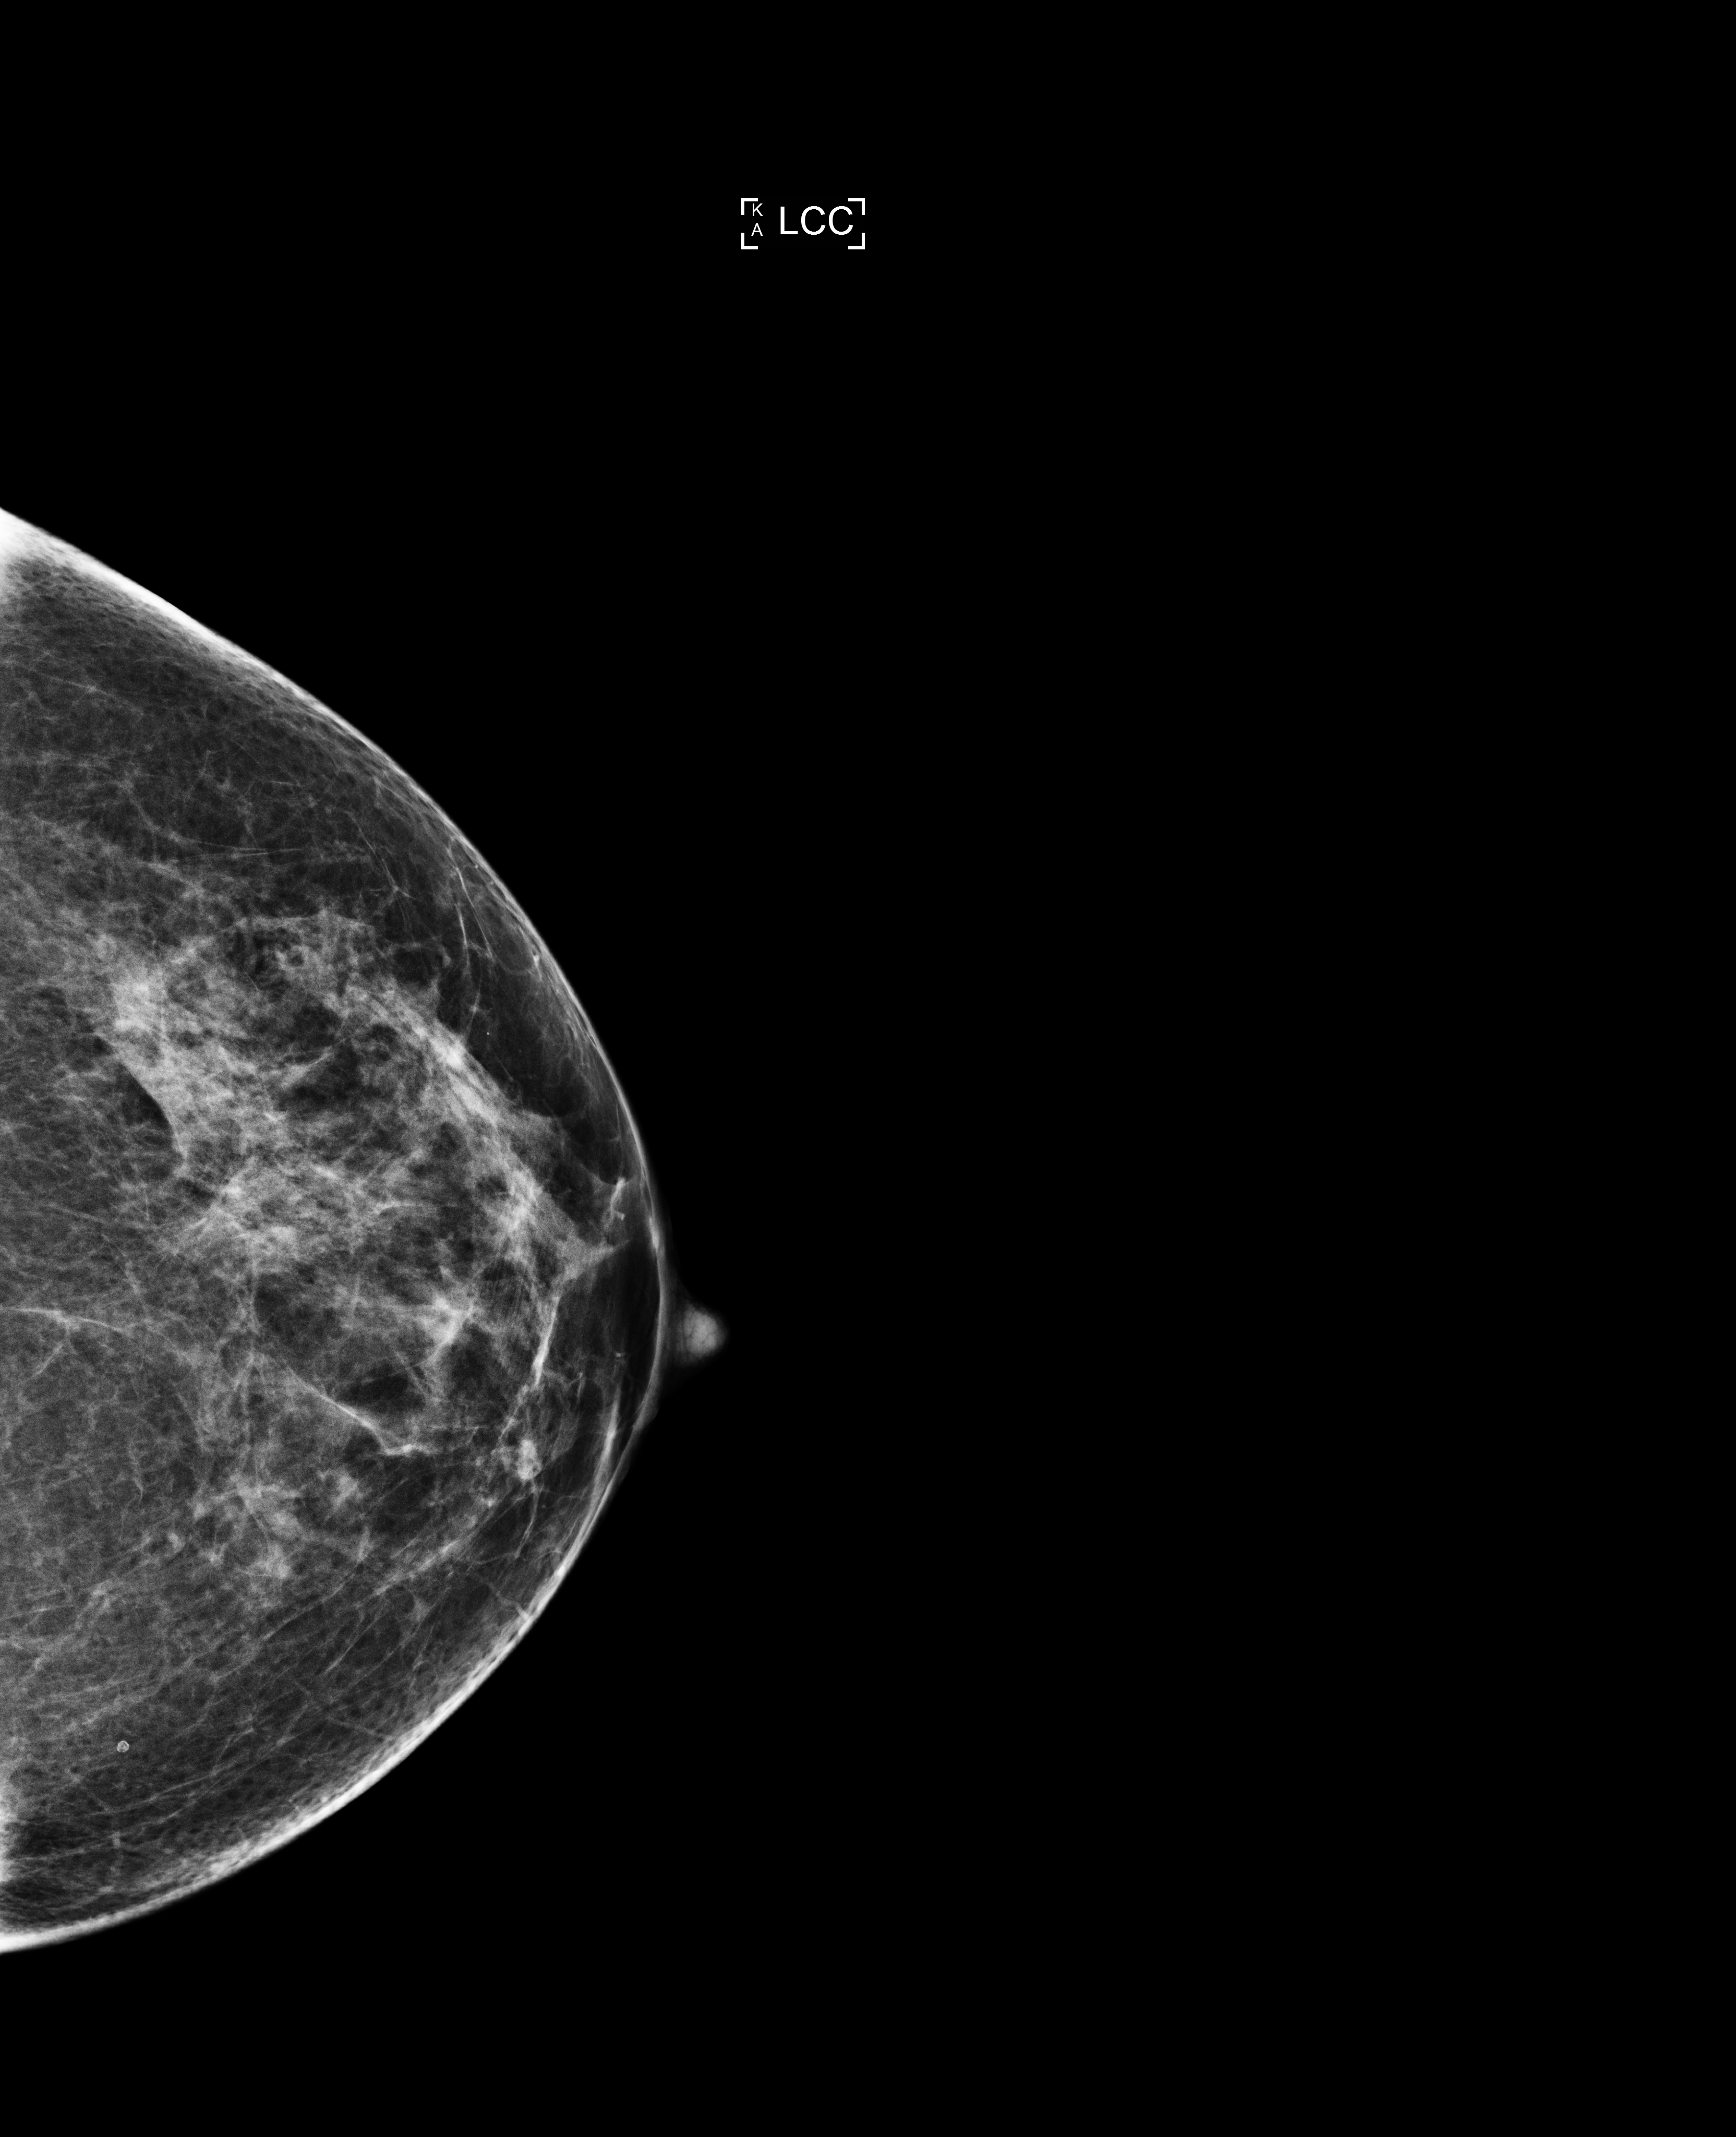
Annual screening mammography examination; compressed breast thickness 59 mm; system: Selenia Dimensions. Patient aged 52 years (female).
Image type: full-field digital mammogram. Breast: left. Projection: craniocaudal (CC) view.